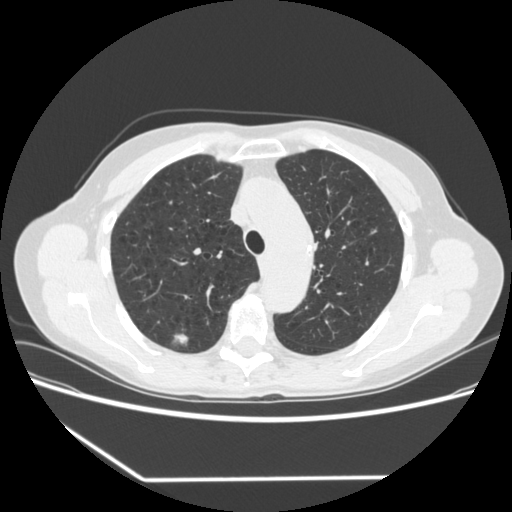
Low-dose screening chest CT, one axial slice; position 248 of 323 along the scan axis; reconstruction kernel STANDARD; 120 kVp; lung window (W 1500 / L -600 HU); 1.25 mm slice thickness; 512 × 512 image matrix.
Structures marked on this image (expert manual segmentation):
- lesion 1 (tumor, upper lobe of right lung): bounding box <174,334,188,344> (left, top, right, bottom; pixels)